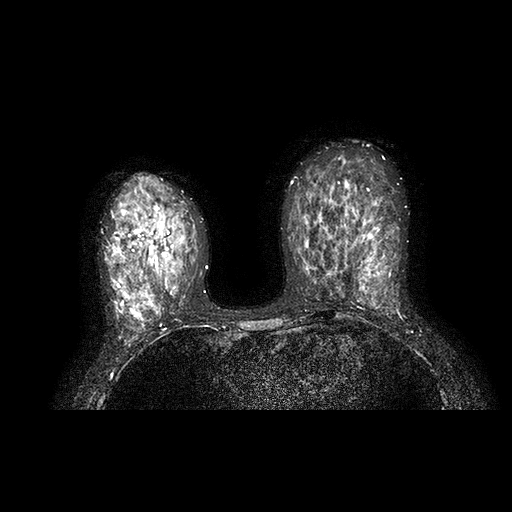
Breast MRI examination; 2 images, each one mid-volume slice chosen by position. Age decade 40s.
Image 1: axial T2-weighted / STIR image, series "T2 STIR AX SENSE", slice 48 of 95, 2 mm slice thickness.
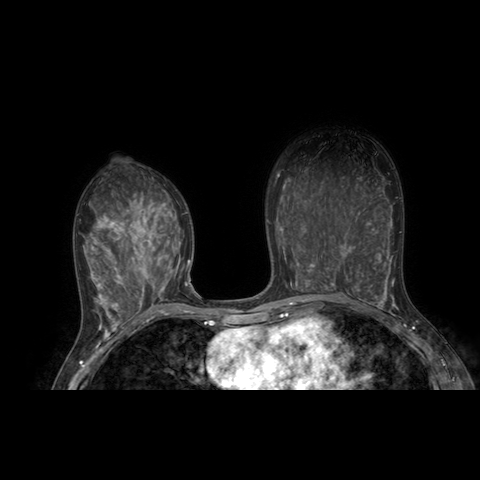
Image 2: axial dynamic contrast-enhanced T1-weighted image, slice 46 of 90, dynamic phase 5 of 8, 4 mm slice thickness.
MRI impression (as recorded): LEFT BREAST: There is moderate background enhancement. In the central to 6:00 location approximately 2 cm anterior to the chest wall, is an oval shaped mass measuring 10 mm ( SE 701 SL 57.9). The enhancement dynamics is progressive persistent. There is no signal on the T2 weighted images of this mass. No masses are noted in any other region of the breast. RIGHT BREAST: There is moderate background enhancement. 1. There is extensive non-mass, heterogeneous enhancement in the upper inner quadrant extending for 7 cm (AP) and 5 cm (SI) dimensions (SE 701 SL 81). 2. There is a spiculated enhancing mass in the 12:00 location mid-breast that is at the lateral extent of the non-mass enhancement. This mass measures 12 x 12 mm (SE 701, SL 87; SE 605, SL 102). A signal void from a biopsy clip is at the lateral margin of this mass. 3. In this same plane in the 12:00 location but posteriorly near the chest wall is a large area of non-mass, heterogeneous enhancement. A signal void at the most inferior edge of this enhancementis noted. 4. In the upper outer quadrant, there is another large spiculated mass with surrounding parenchymal enhancement that measures approximately 32
x 32 mm (SE 701 SL 100.5; SE 605 SL 112).
5. There is non-specific, non-mass enhancement extending into the
inferior breast centrally- to 6:00 location near the chest wall.
7. Lymph nodes are very posterior in location, and are therefore
incompletely visualized.
IMPRESSION:
1) Findings most consistent with multicentric malignancy involving all four quadrants of the RIGHT breast , as documented by the two core biopsies. Cannot rule out lymphadenopathy, which may be non-specific since this study was performed post-core biopsies.
2) Suspicious solitary 1 cm mass in the LEFT in spite of kinetics since
it is a solitary finding. In spite of the T2 findings, this may represent a fibroadenoma due to its morphology, but malignancy cannot be ruled out; BI-RADS 4B.
Patient-level pathology facts (from the clinical record, not from the images): pathology diagnosis: INVASIVE DUCTAL CARCINOMA (right breast); pathology report notes: RIGHT BREAST AND AXILLARY CONTENTS
HISTOLOGIC TYPE: INVASIVE DUCTAL CARCINOMA. SIZE OF INVASIVE COMPONENT: TWO FOCI, 1.3cm AND 1.9cm IN GREATEST DIMENSION RESPECTIVELY HISTOLOGIC MODIFIED SCARF BLOOM RICHARDSON GRADE: II/III EXTENSIVE INTRADUCTAL CARCINOMA (EIC): ABSENT MICROCALCIFICATIONS:PRESENT IN BOTH TUMOR AND NONNEOPLASTIC TISSUE
SKIN/DERMAL LYMPHATICS INVASION: ABSENT No regional lymph node metastasis histologically.